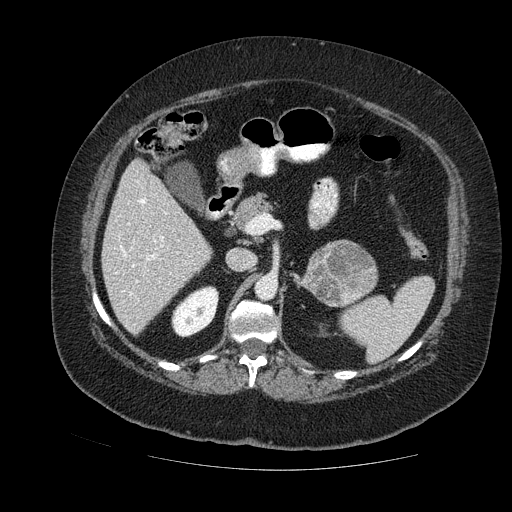
Contrast-enhanced abdominal CT, one axial slice; position 69 of 121 along the scan axis; soft-tissue window (W 400 / L 40 HU); 512 × 512 image matrix. Female patient. Case-level facts recorded for this patient, not image findings: diagnosis: adrenocortical carcinoma; tumour side: left adrenal; tumour size at pathology: 8 cm; Ki-67 index: 7 %; stage (as recorded): 2.
Structures marked on this image (semi-automatic segmentation, software-assisted and operator-edited):
- mass: bounding box <304,243,375,307> (left, top, right, bottom; pixels)